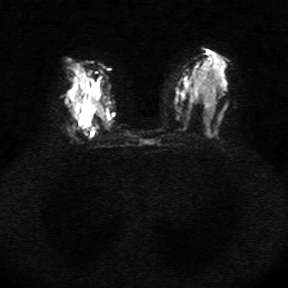
Breast MRI, one axial slice; slice 15 of 34 in the series (ordered by position); diffusion-weighted series; image 2 of 4 stored at this slice position (different b-values; order by instance number); 1.5 T; 5 mm slice thickness; 288 × 288 image matrix. Female patient.
Annotated regions visible in this slice (expert manual segmentation):
- tumour on diffusion-weighted imaging: bounding box [x1, y1, x2, y2] px = [79, 111, 92, 120]